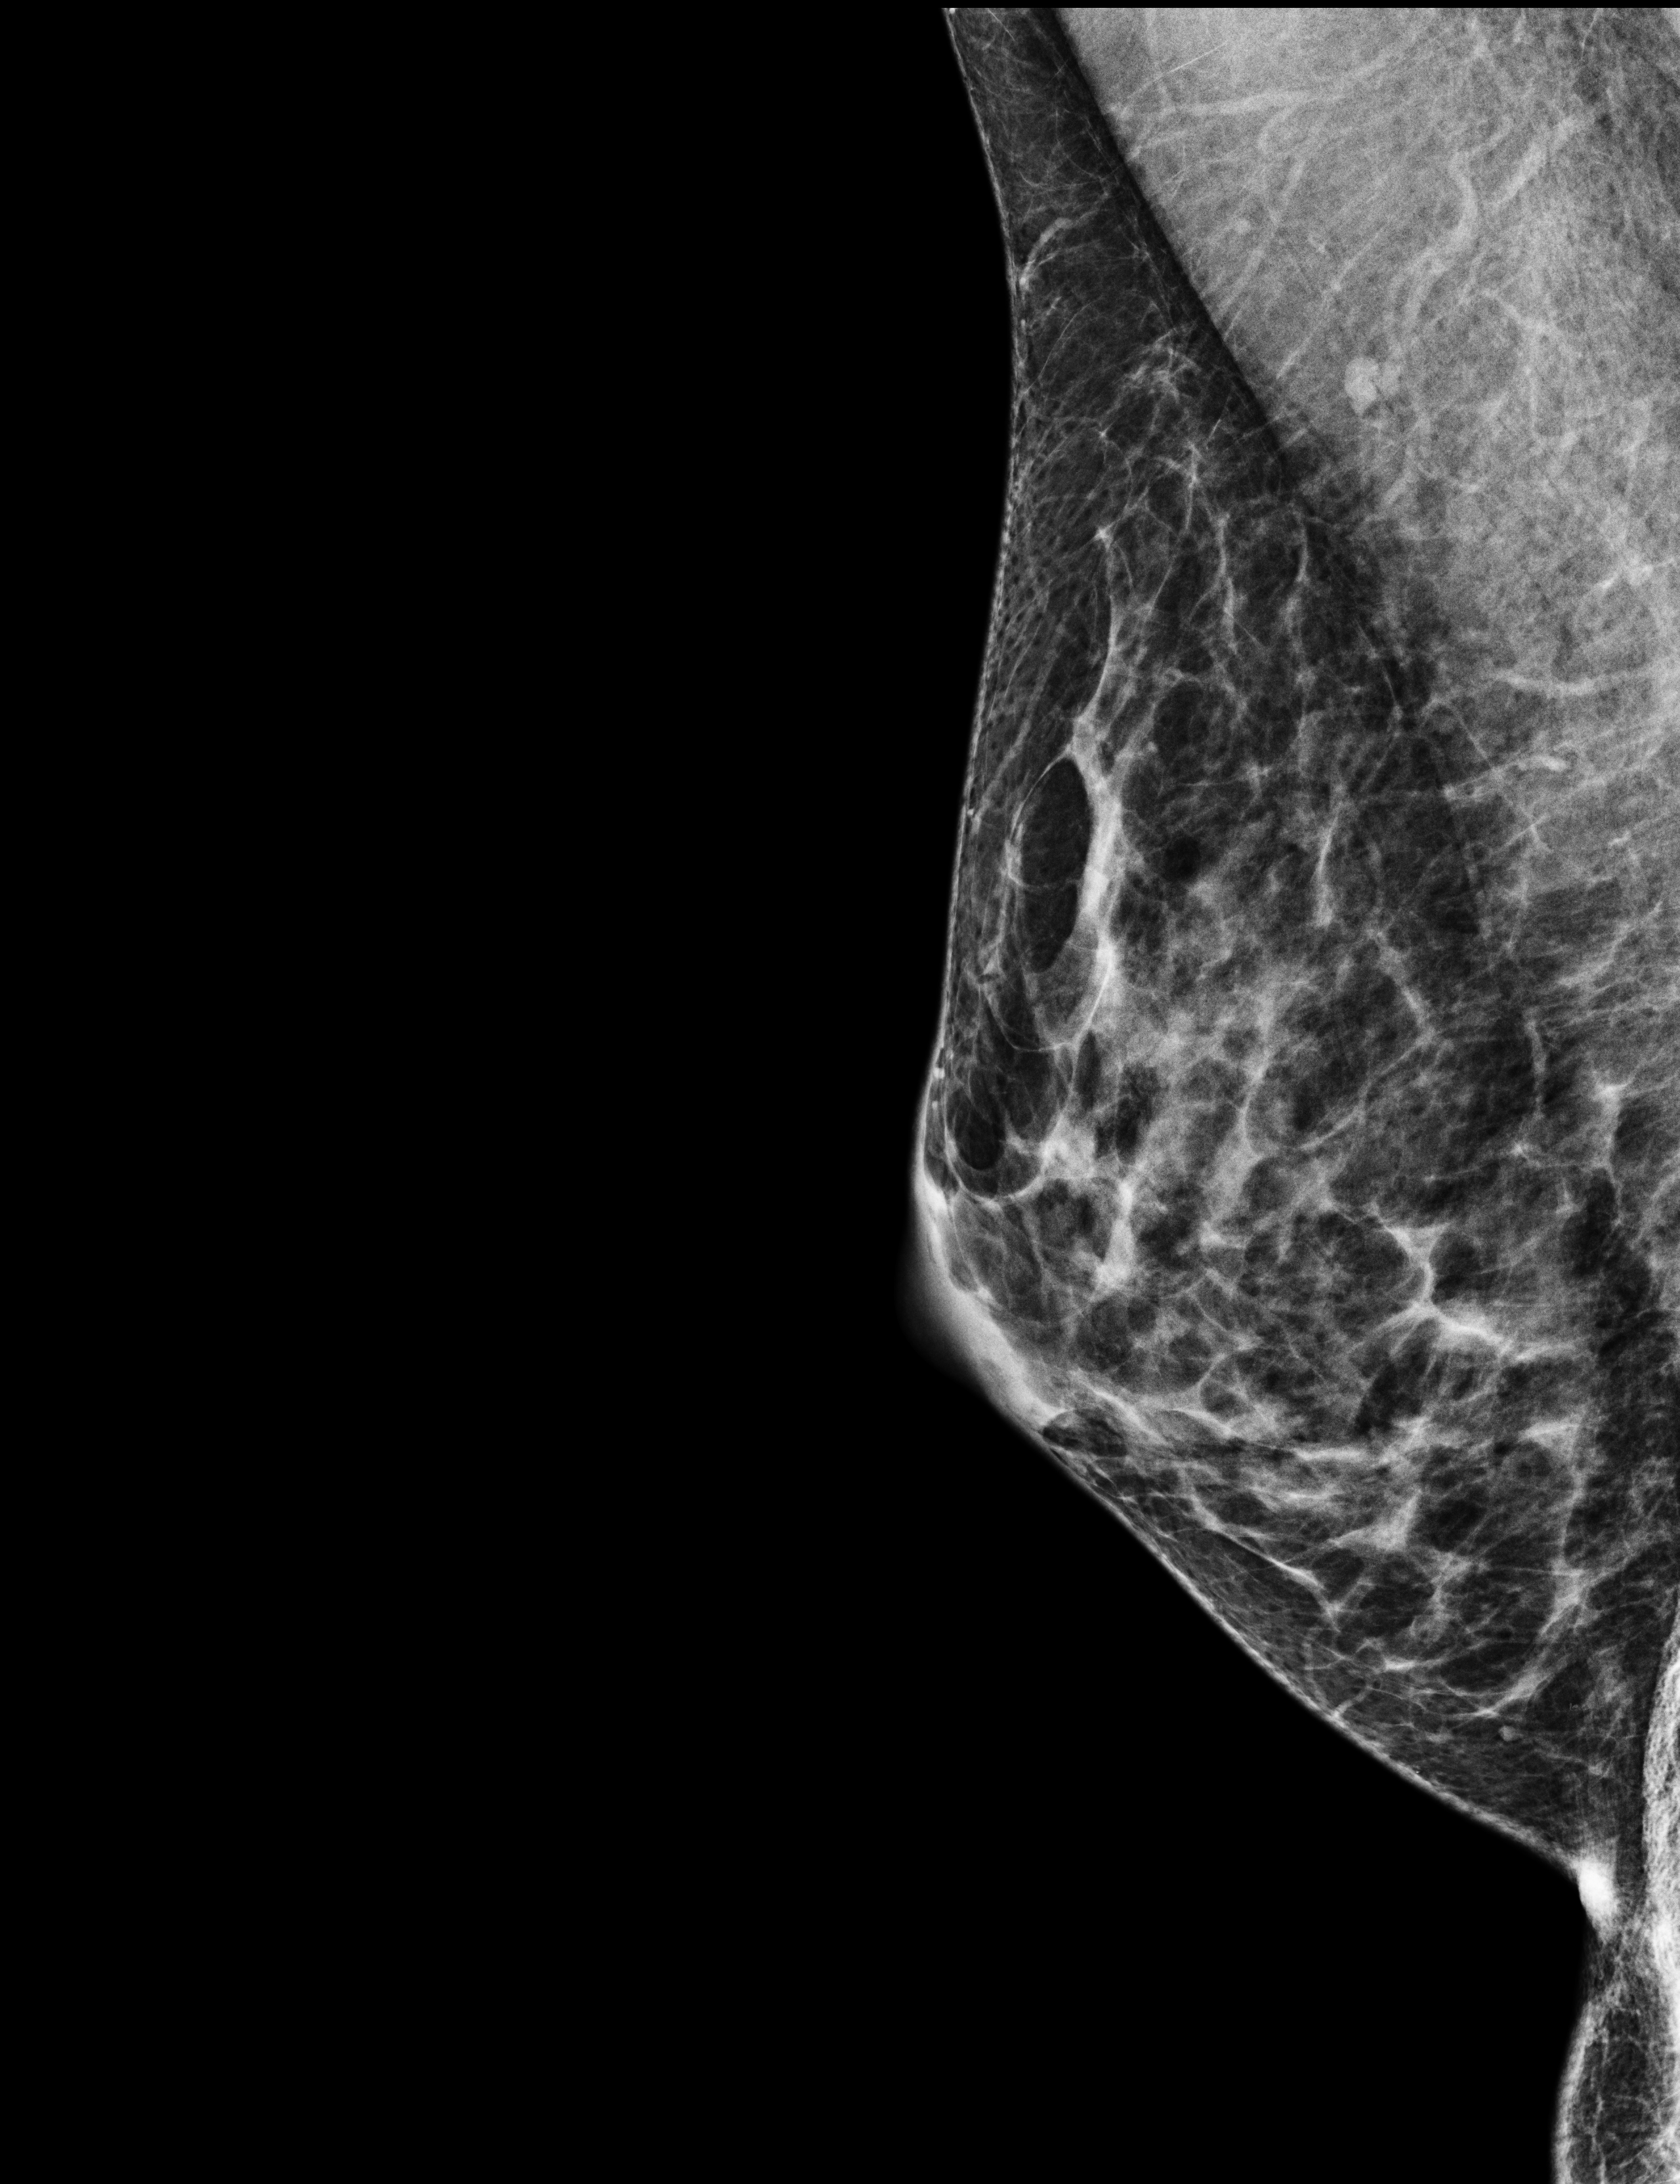
Full-field digital mammogram (FFDM), right breast, mediolateral oblique (MLO) view, screening examination. Patient aged 51 years (female).
Breast density at the screening exam (both breasts): heterogeneously dense (BI-RADS density category c). Final BI-RADS category for the screening round (tomosynthesis exam, both breasts): category 1. Recall: no recall after this screen.